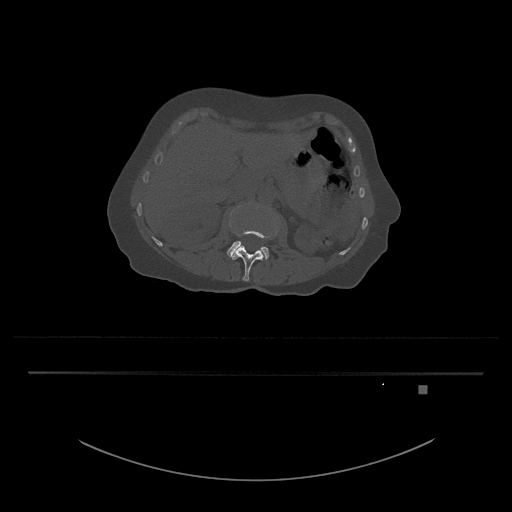
CT including the spine, one axial slice; position 470 of 797 along the scan axis; reconstruction kernel Br40s/3; bone window (W 1800 / L 400 HU); 0.5 mm slice thickness; 512 × 512 image matrix, field of view 500 × 500 mm. Patient: female, 57 years. Case-level facts recorded for this patient, not image findings: primary cancer: cervical.
Structures marked on this image (semi-automatically segmented with operator editing):
- L3 vertebra: bounding box <227,205,277,259> (left, top, right, bottom; pixels)